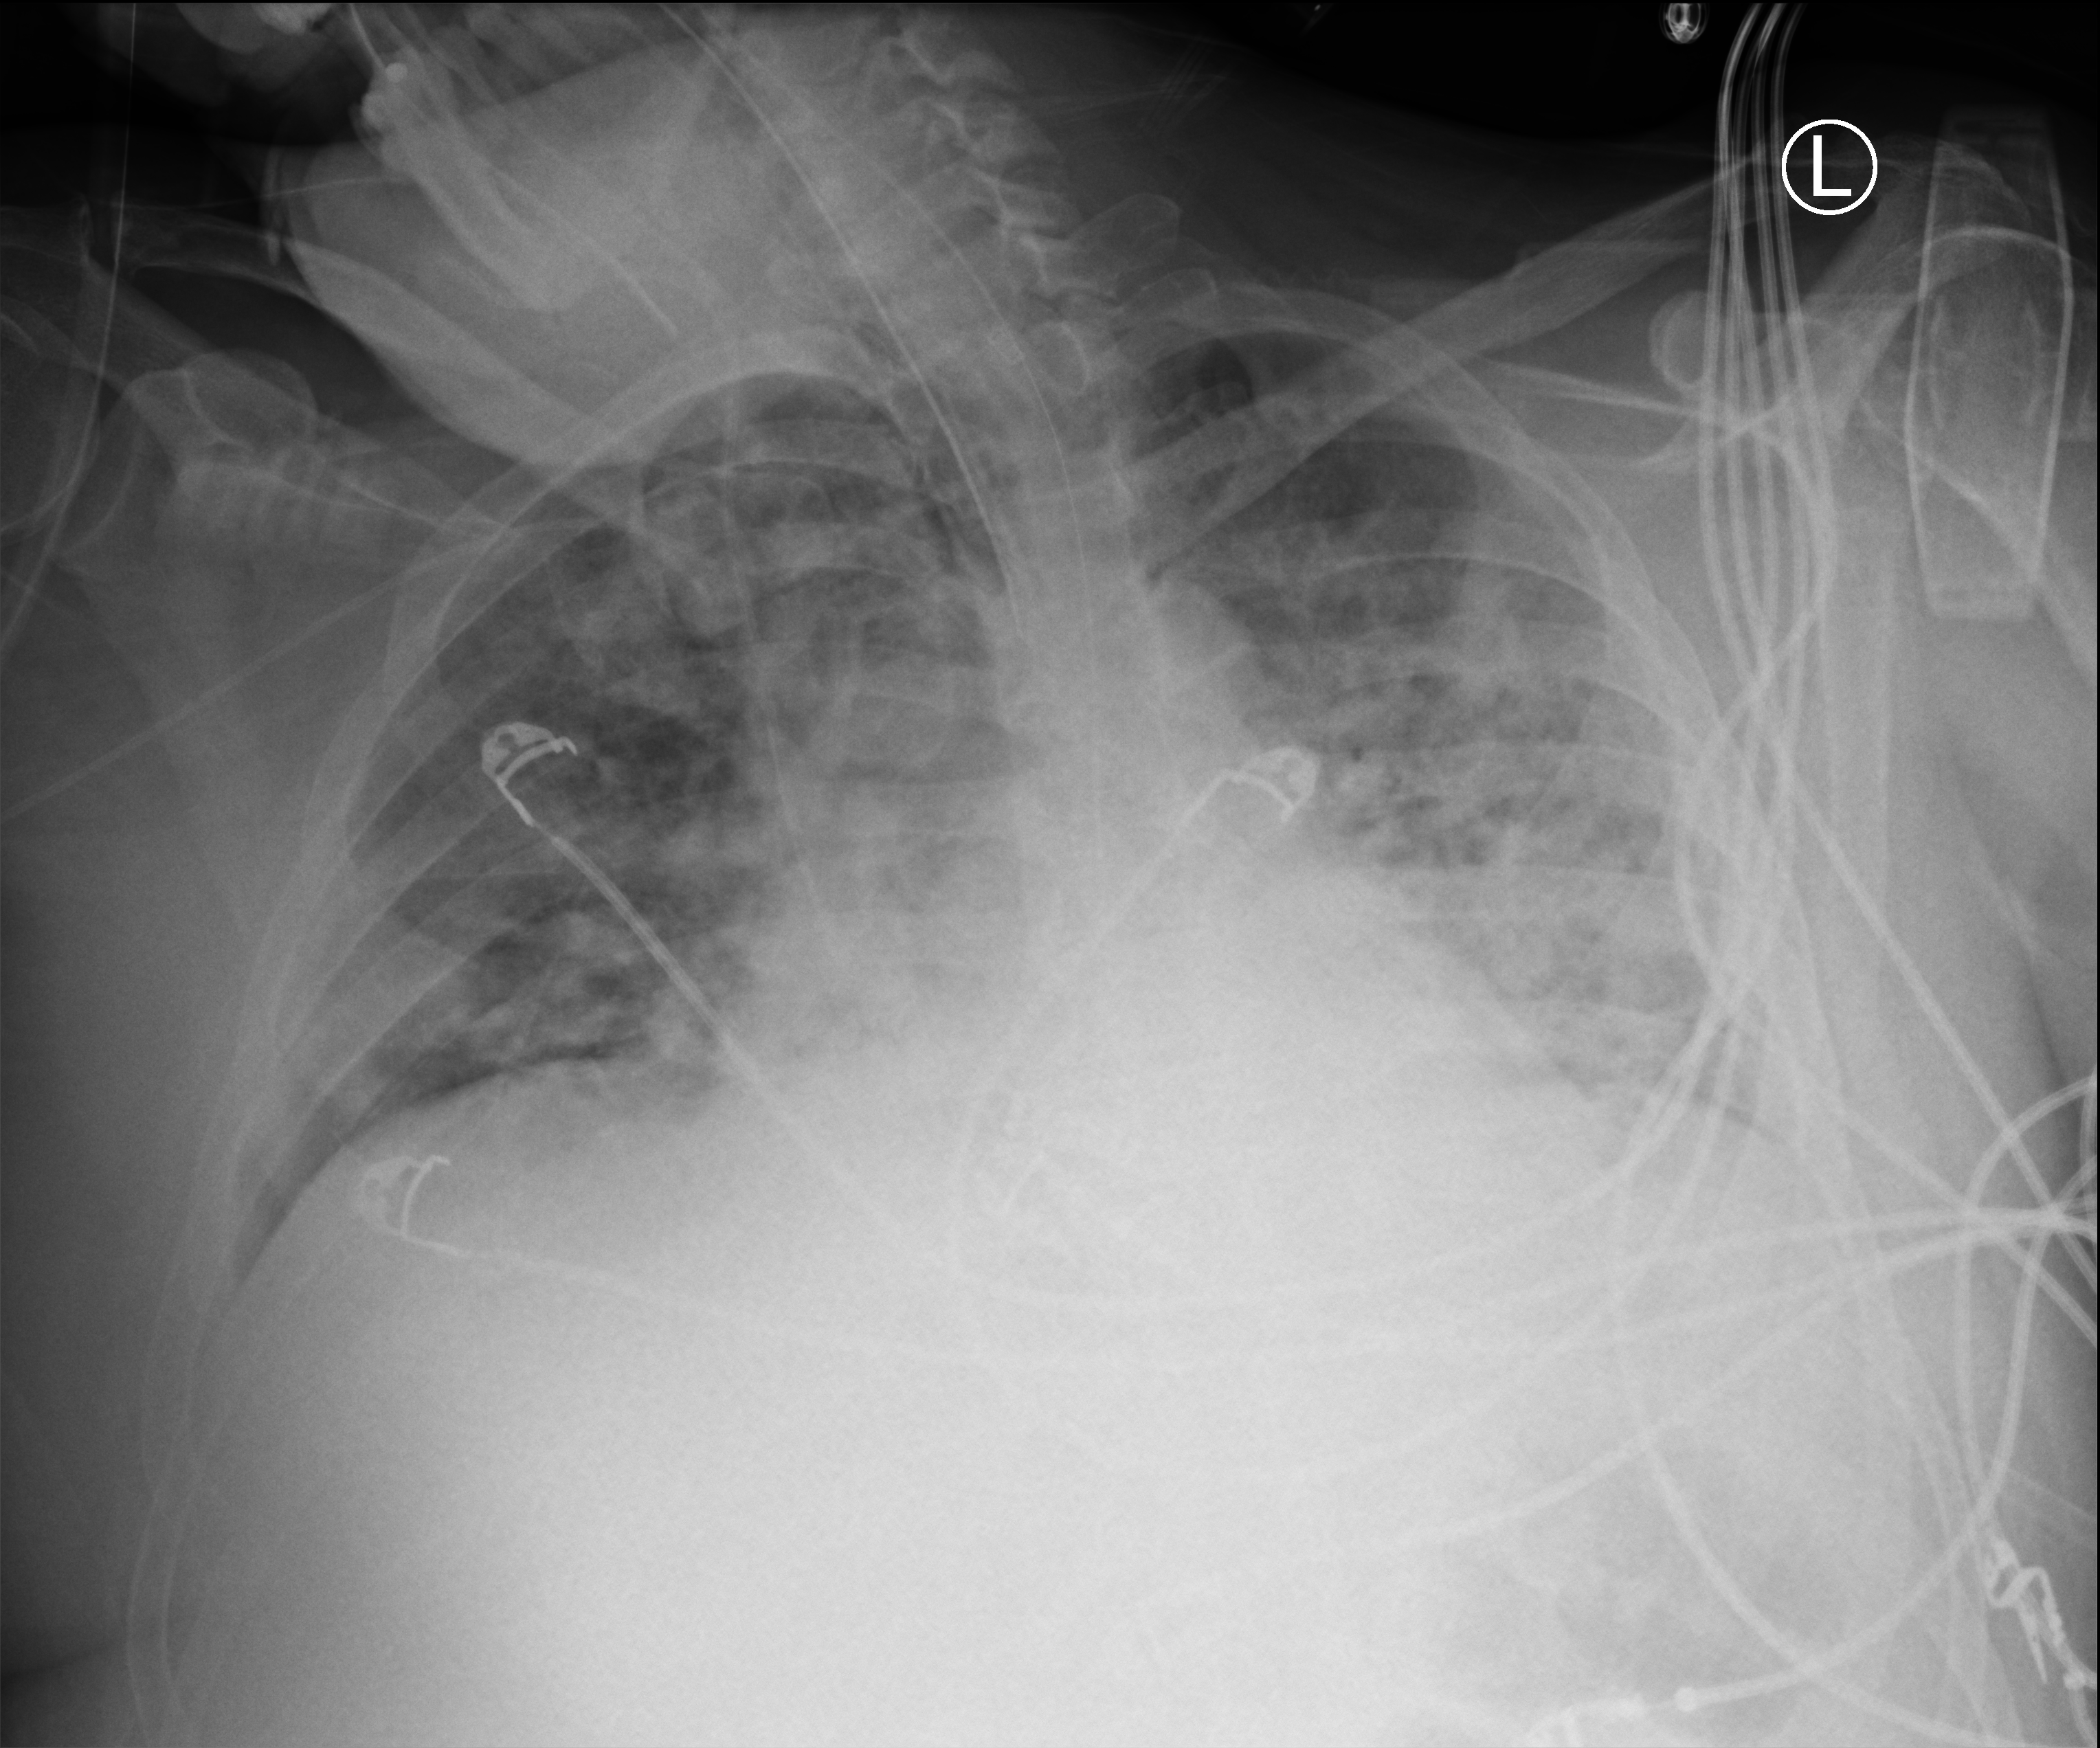
Bedside chest radiograph (computed radiography); anteroposterior (AP) projection. Male patient hospitalised with COVID-19, age 18–59 years.
Admission-level facts for this patient (not findings on this image; timing relative to this image not recorded): mechanically ventilated during this hospital stay: yes; admitted to intensive care during this hospital stay: yes; smoking status (admission record): former.